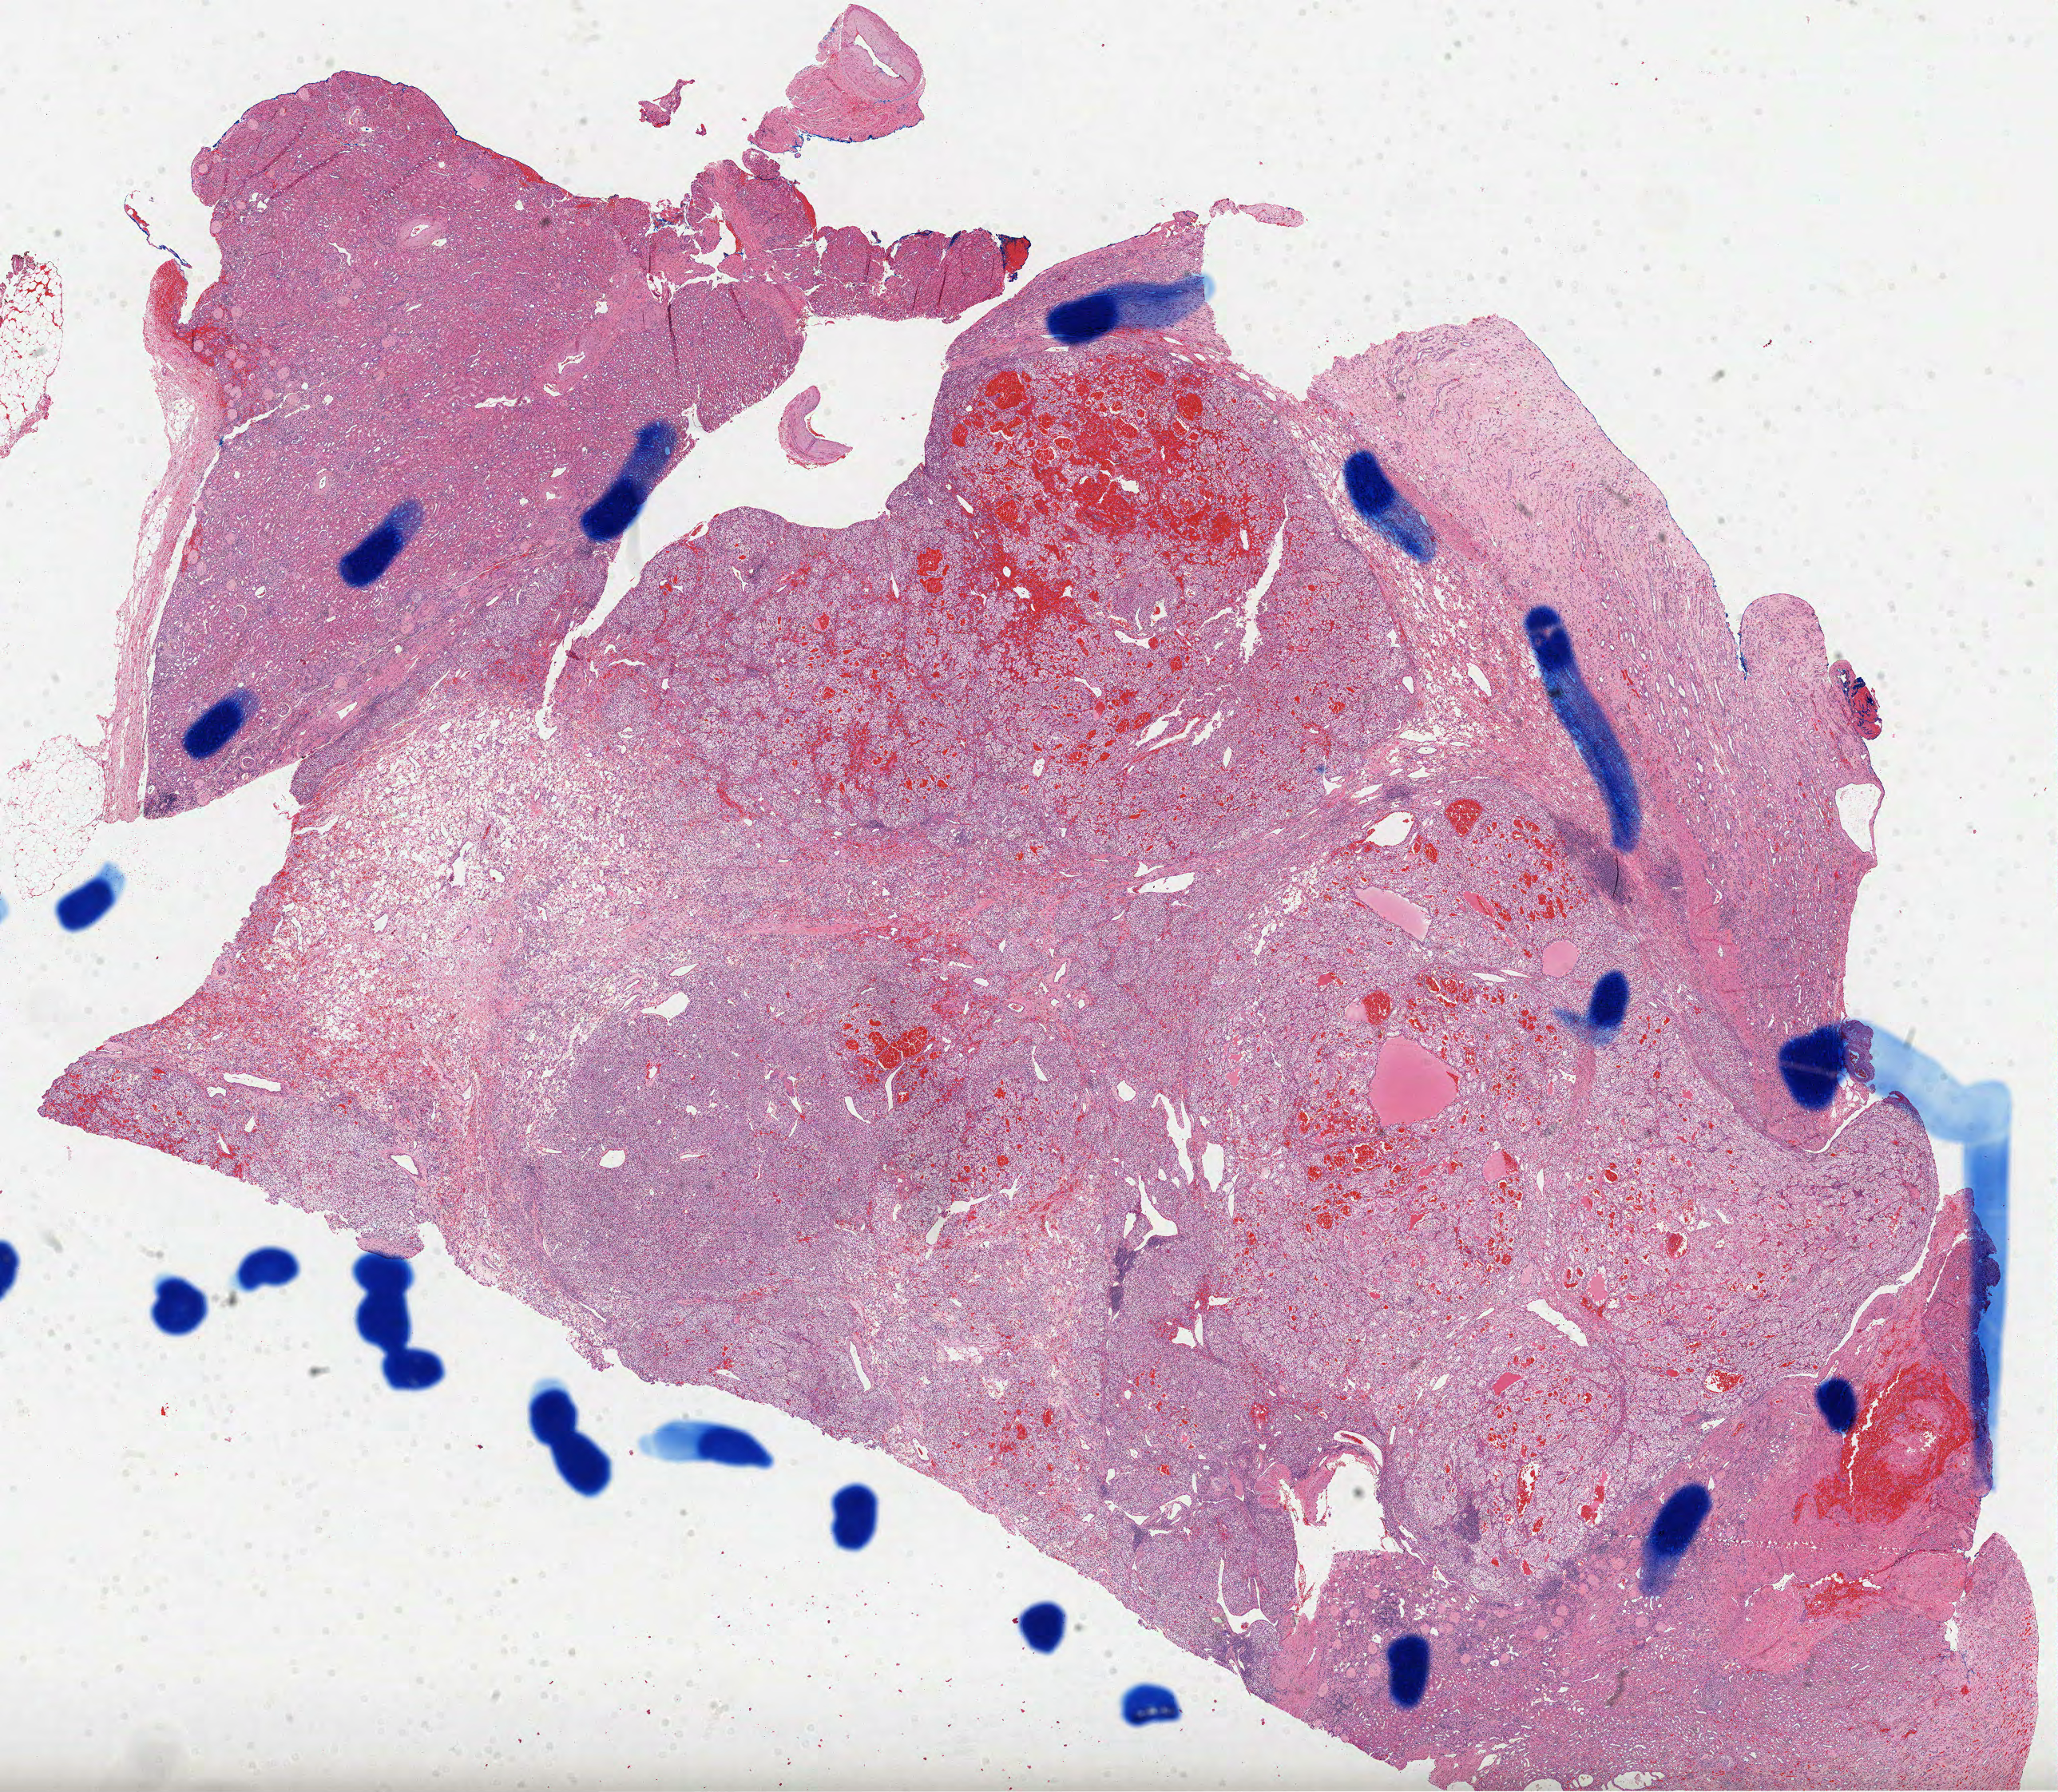
Whole-slide histology image, H&E, whole scanned area (about 20.8 x 18.1 mm) shown as a low-resolution overview. Formalin-fixed paraffin-embedded (FFPE) diagnostic section. Primary tumour sample from the kidney. Female, age 71 years at initial diagnosis. Histologic grade: G2 (moderately differentiated).
Pathologic diagnosis: Clear cell adenocarcinoma, NOS. AJCC pathologic stage: I (6th edition). TNM: T1a N0 M0.